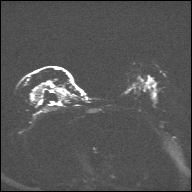
Breast MRI, one axial slice. Slice 23 of 32 in the series (ordered by position). Diffusion-weighted series; image 2 of 4 stored at this slice position (different b-values; order by instance number). 1.5 T. 4 mm slice thickness. 192 × 192 image matrix. Female patient.
Outlined on this slice (outlined manually by an expert reader):
- tumour on diffusion-weighted imaging: box from (x=35, y=81) to (x=57, y=101) px